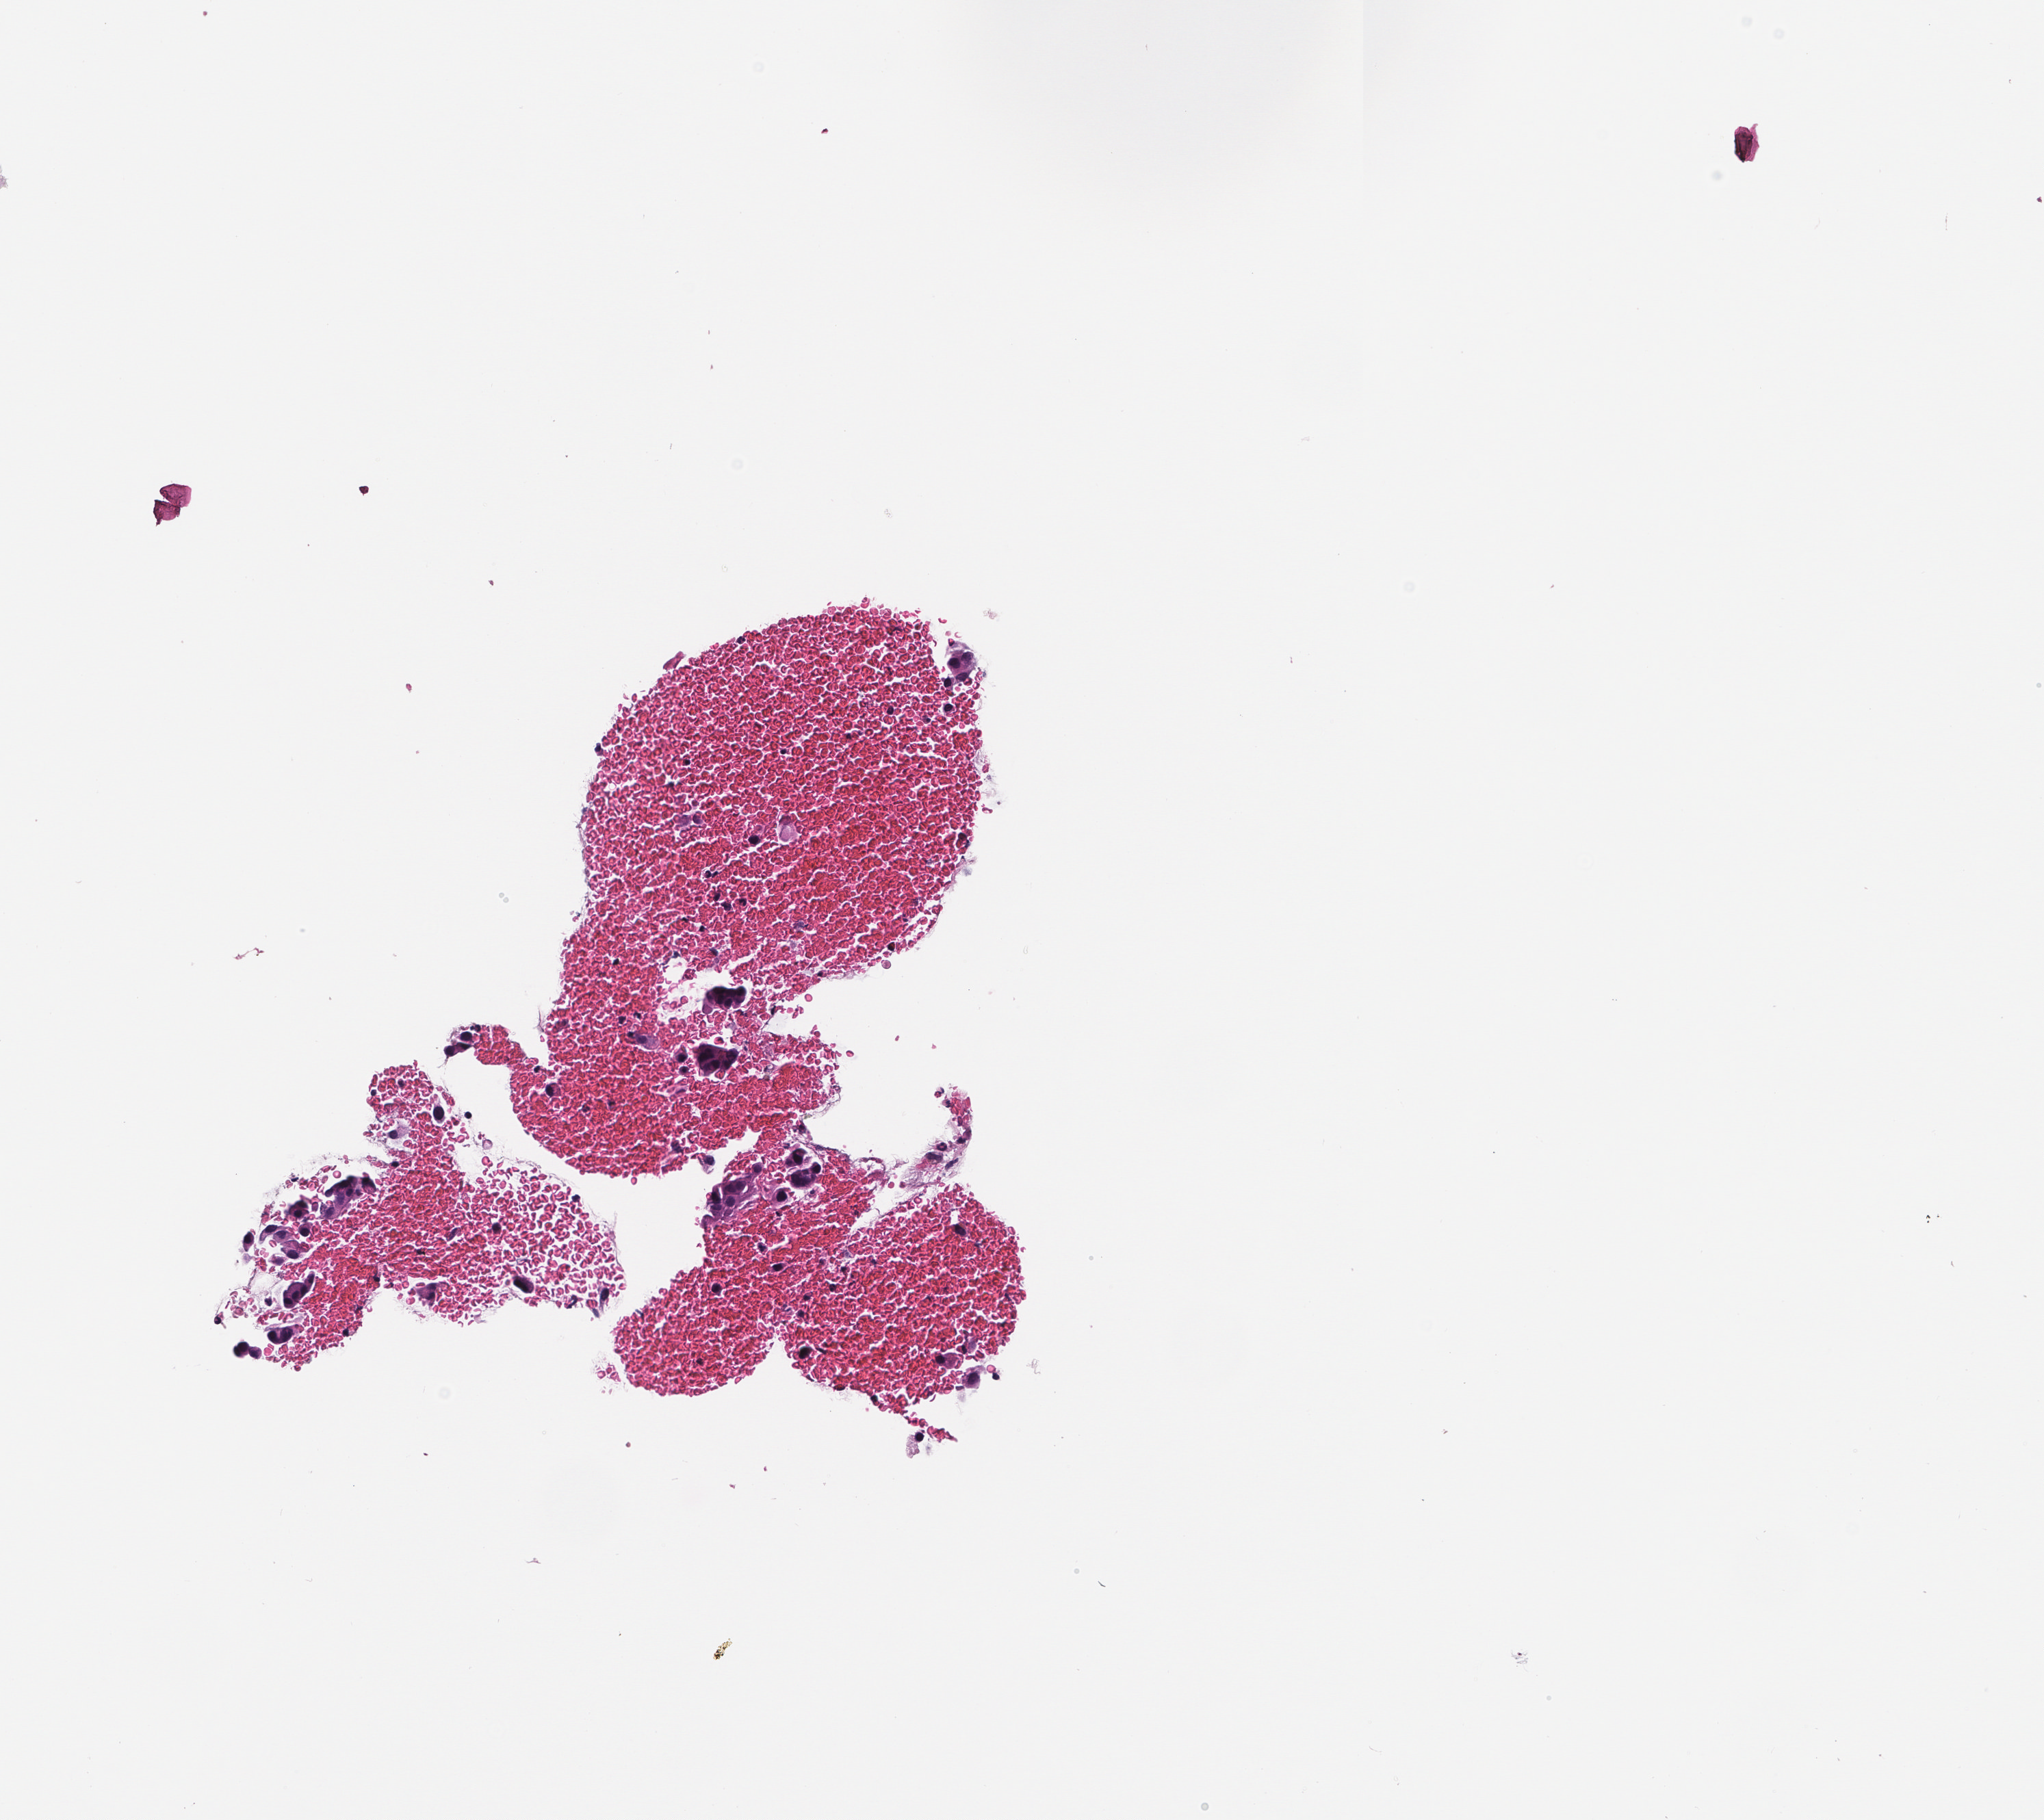
Haematoxylin and eosin whole-slide image — whole scanned area (about 1.5 x 1.3 mm) shown as a low-resolution overview. FFPE section. Tissue site: lung. Patient: male.
This section: primary tumour tissue. Diagnosis: Non-Small Cell Lung Carcinoma.